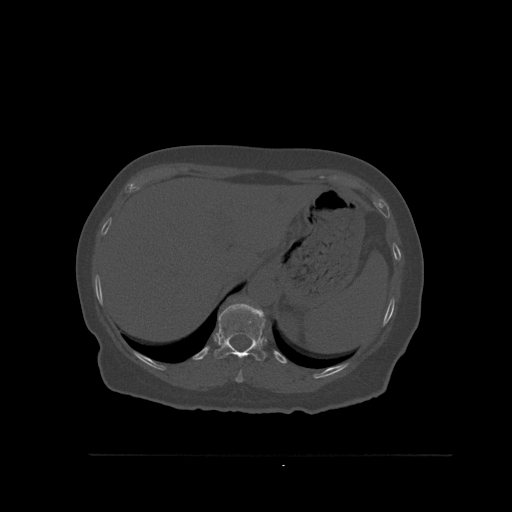
CT including the spine, one axial slice. Slice 304 of 527 in the series (ordered by position). Bone window (W 1800 / L 400 HU). 512 × 512 image matrix, field of view 470 × 470 mm. Female patient, age 73 years. From the clinical record (not read from this slice): primary cancer: breast; vertebrae with lytic lesions (as recorded): L2.
Outlined on this slice (semi-automatic segmentation, software-assisted and operator-edited):
- T10 vertebra: bounding box <235,370,244,383> (left, top, right, bottom; pixels)
- T11 vertebra: <213,303,267,361>